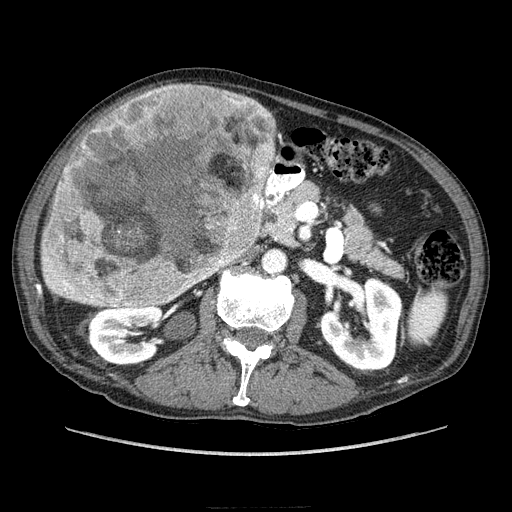
Contrast-enhanced abdominal CT (liver protocol), one axial slice; slice 109 of 218 in the series (ordered by position); soft-tissue window (W 400 / L 40 HU); 512 × 512 image matrix, field of view 380 × 380 mm. Case-level facts recorded for this patient, not image findings: diagnosis: hepatocellular carcinoma (patient treated with transarterial chemoembolisation; whether this scan precedes or follows treatment is not stated here); TNM stage (as recorded): Stage-IIIA; Child-Pugh class: A; tumour nodularity: multinodular.
Annotated regions visible in this slice (semi-automatically segmented with operator editing):
- liver parenchyma outside the tumour (the mass and vessels are separate outlines, so this box may not span the whole liver): box from (x=42, y=90) to (x=317, y=294) px
- mass: (x=42, y=83)–(x=276, y=310)
- liver vessels: (x=276, y=211)–(x=285, y=224)